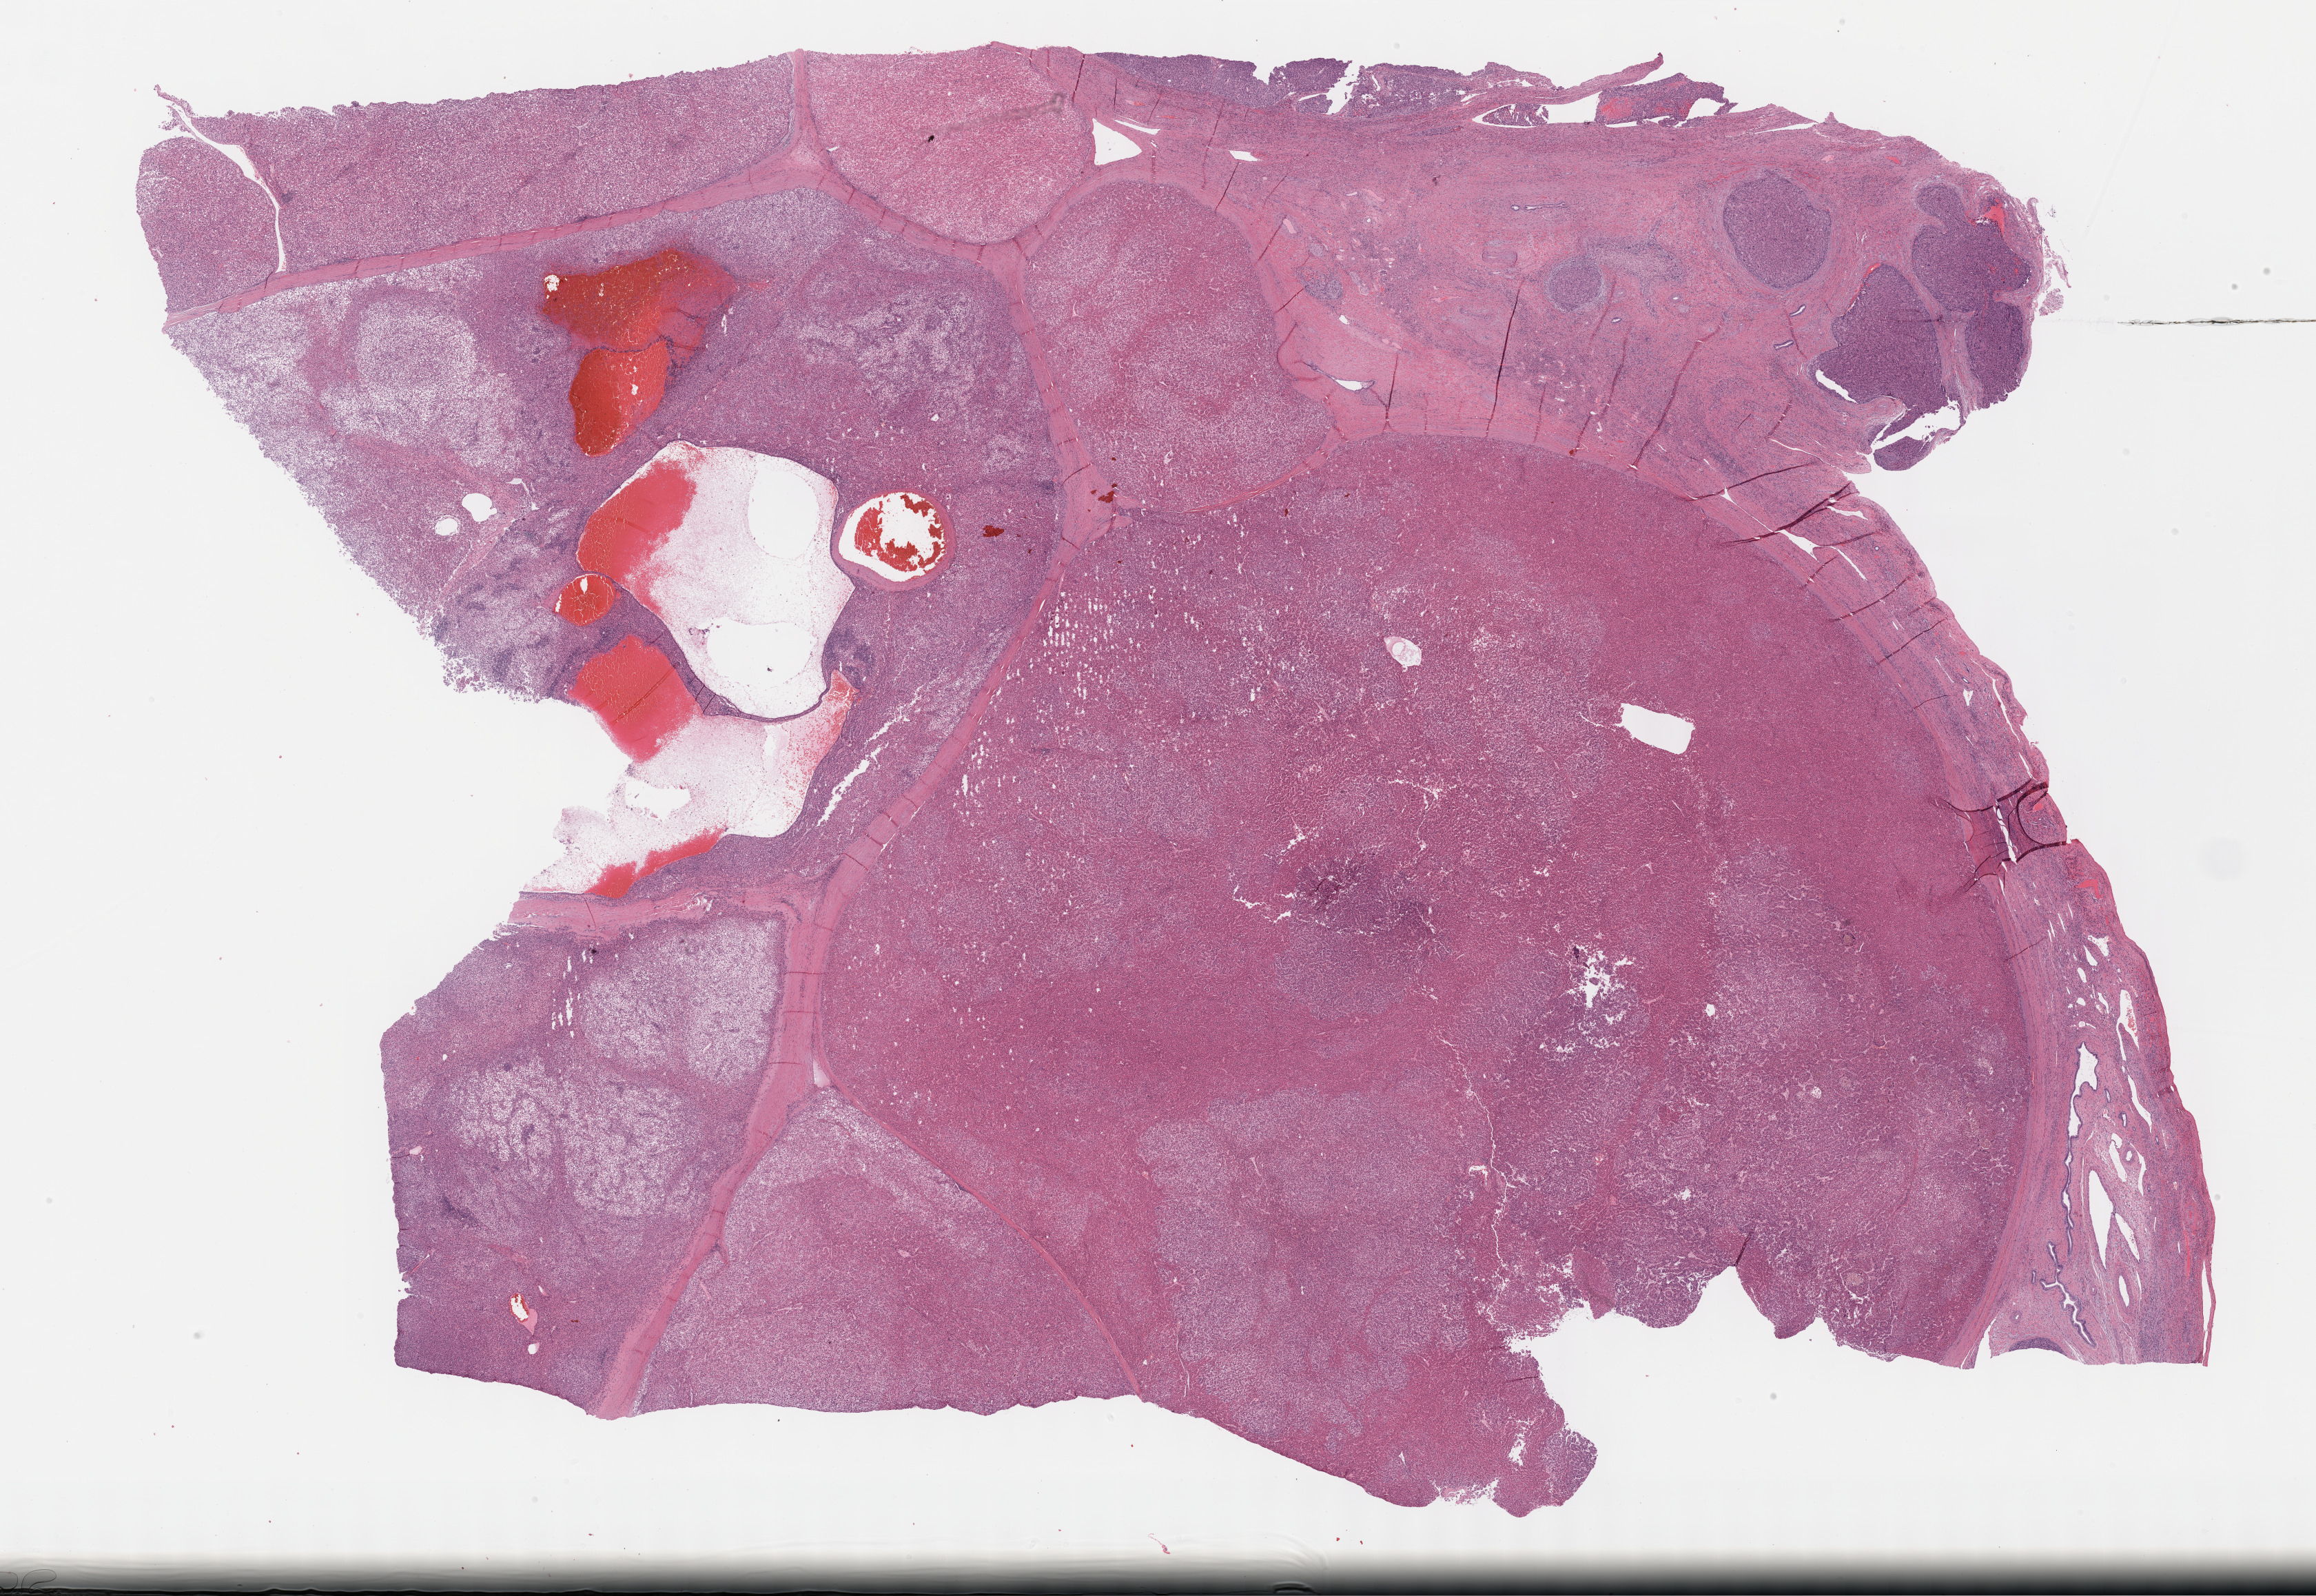
Whole-slide histology image, H&E, low-resolution overview of the scanned area, about 27.2 x 18.7 mm (slide scanned at 40x). FFPE section. Liver, primary tumour sample. Patient: female, age at initial diagnosis 53 years. Histologic grade: G3 (poorly differentiated).
AJCC pathologic stage: IIIA (7th edition). Histologic diagnosis: Hepatocellular carcinoma, NOS.